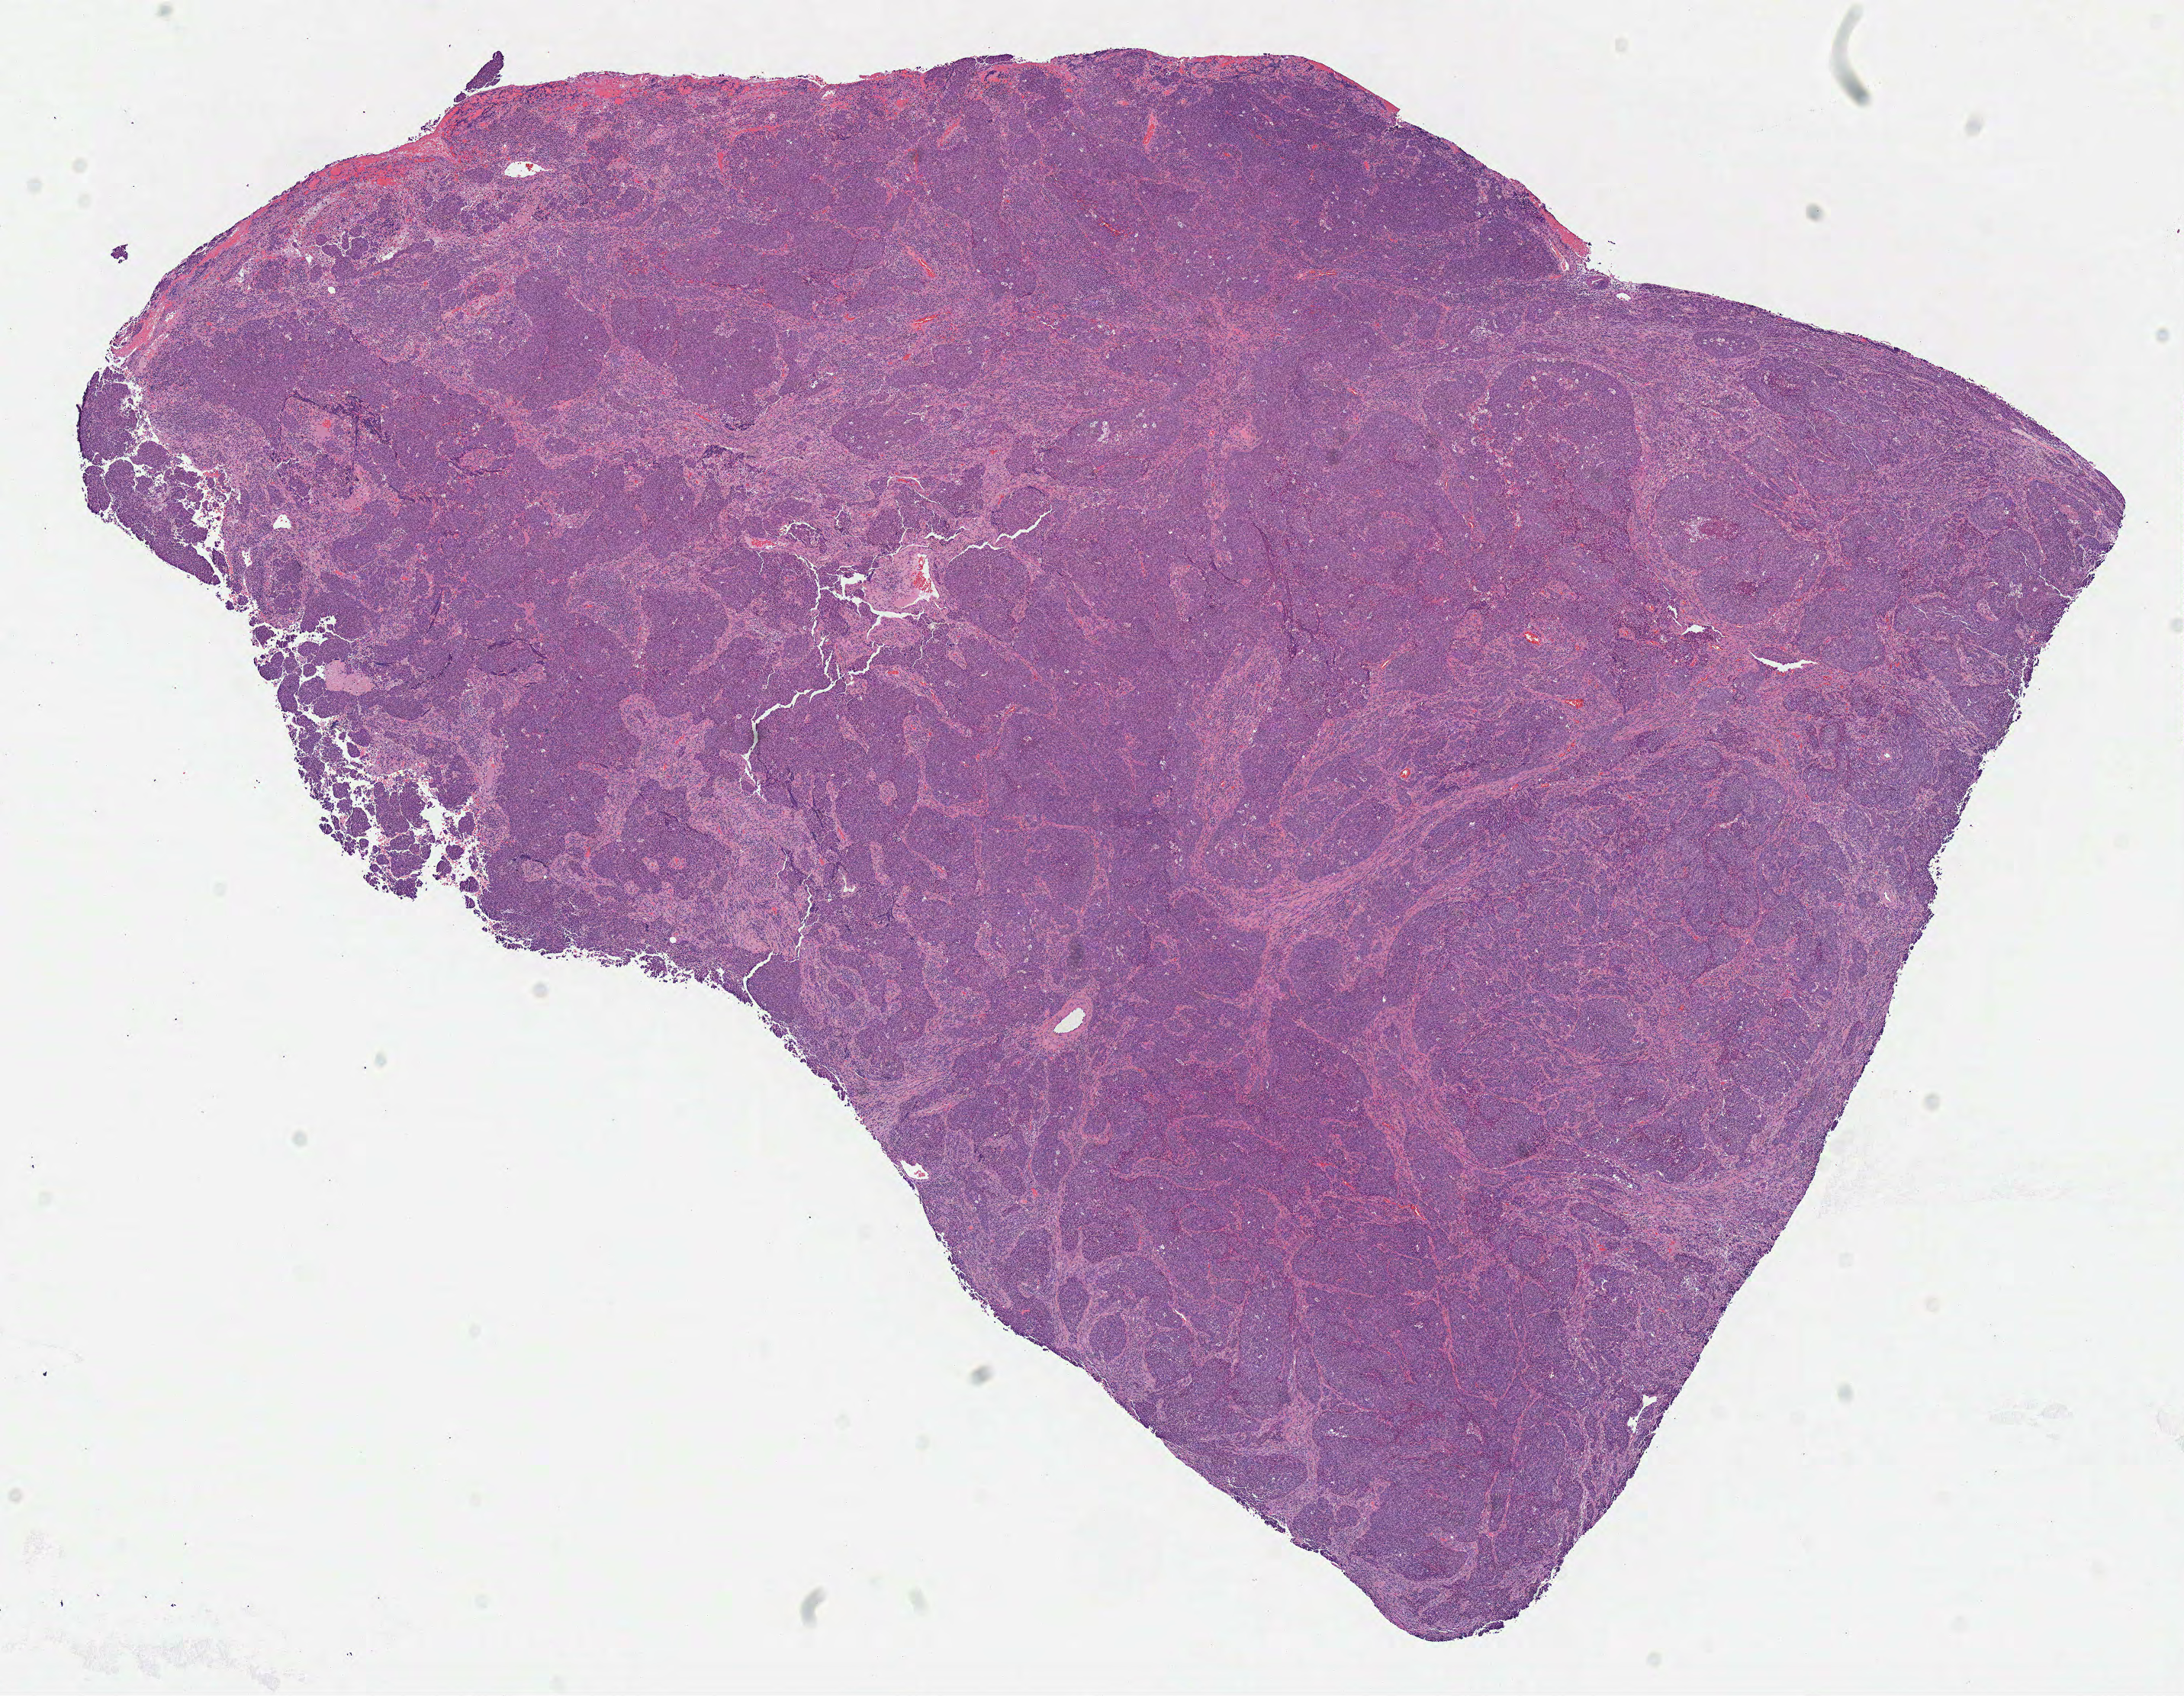
H&E whole-slide image — whole scanned area (about 11.3 x 8.7 mm, from a 40x scan) shown as a low-resolution overview. Formalin-fixed paraffin-embedded (FFPE) diagnostic section. Sample: primary tumour, cervix. Female patient; age at initial diagnosis 28 years. Histologic grade: G3 (poorly differentiated).
• FIGO stage: IIIB
• pathologic diagnosis: Basaloid squamous cell carcinoma
• lymph nodes positive (case pathology): 1 of 24 examined